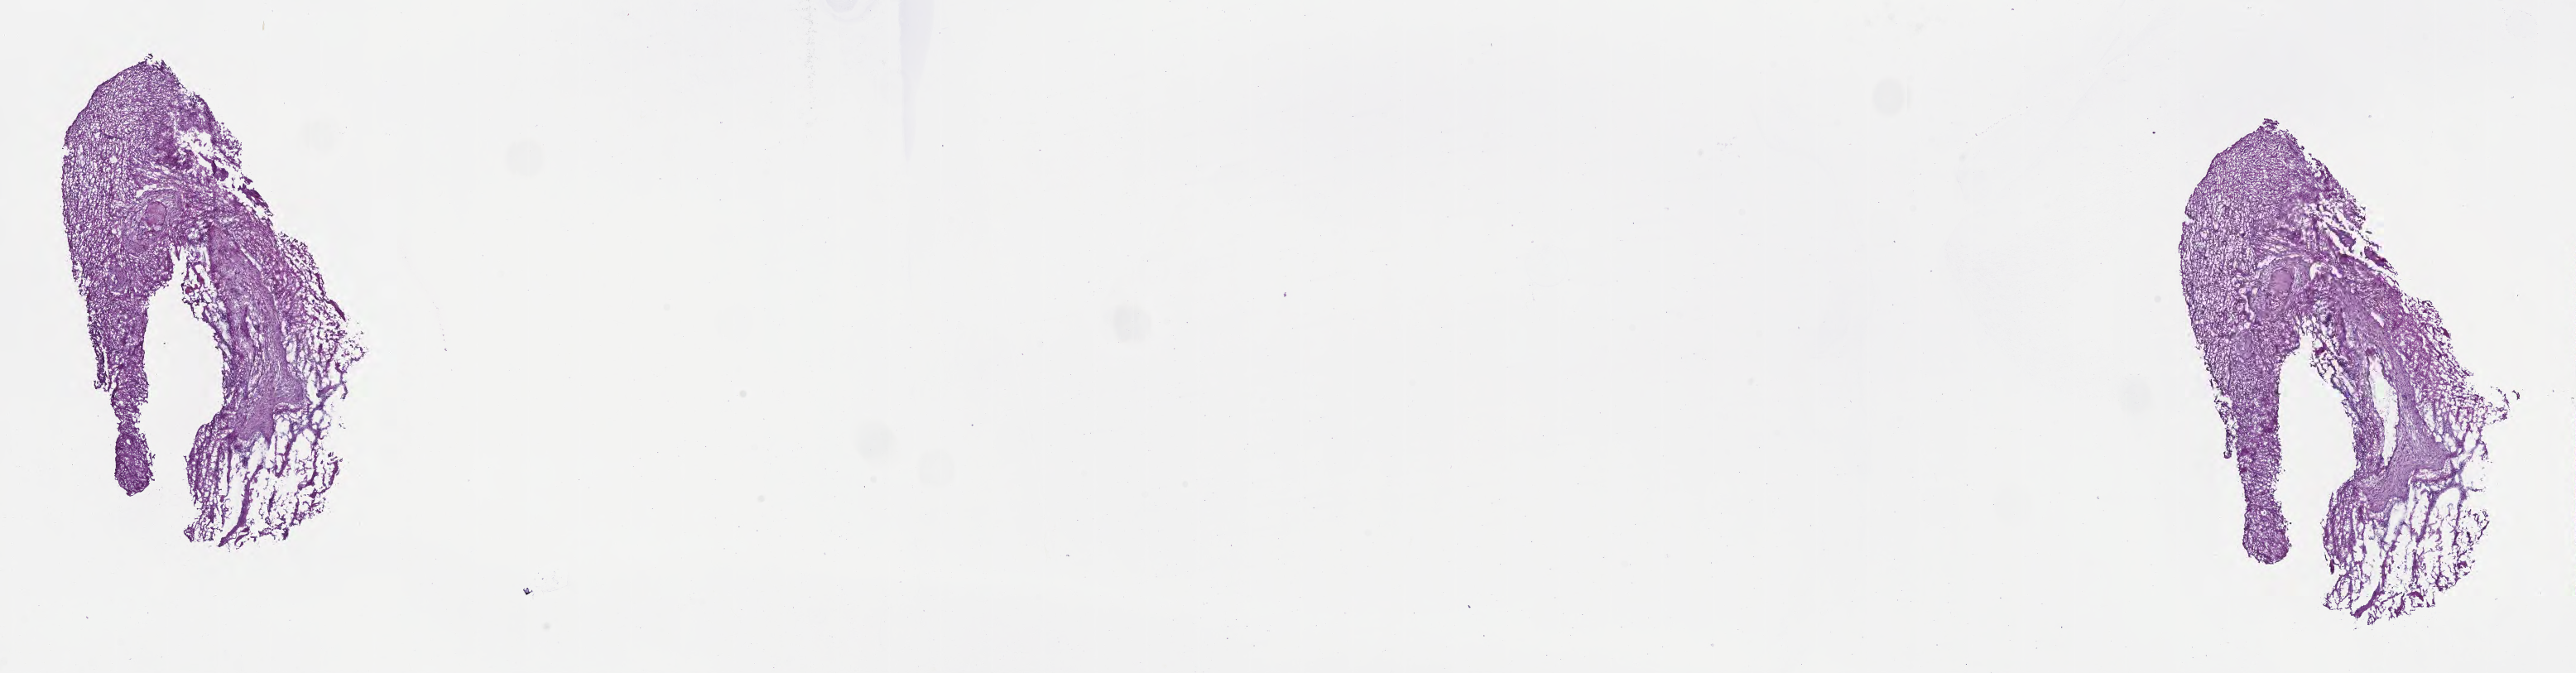
Digitized haematoxylin and eosin-stained section of tumor tissue from the brain — a low-resolution overview of the entire scanned area, about 25.2 x 6.6 mm. Frozen section (OCT-embedded). Patient: female, age 659 days.
Diagnosis: Tumor cells, uncertain whether benign or malignant.